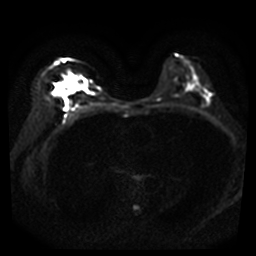
Breast MRI, one axial slice. Position 22 of 40 along the scan axis. Diffusion-weighted series; image 2 of 4 stored at this slice position (different b-values; order by instance number). 3 T. 5 mm slice thickness. 256 × 256 image matrix. Female patient.
Annotated regions visible in this slice (manually delineated by an expert):
- tumour on diffusion-weighted imaging: box from (x=55, y=74) to (x=75, y=96) px